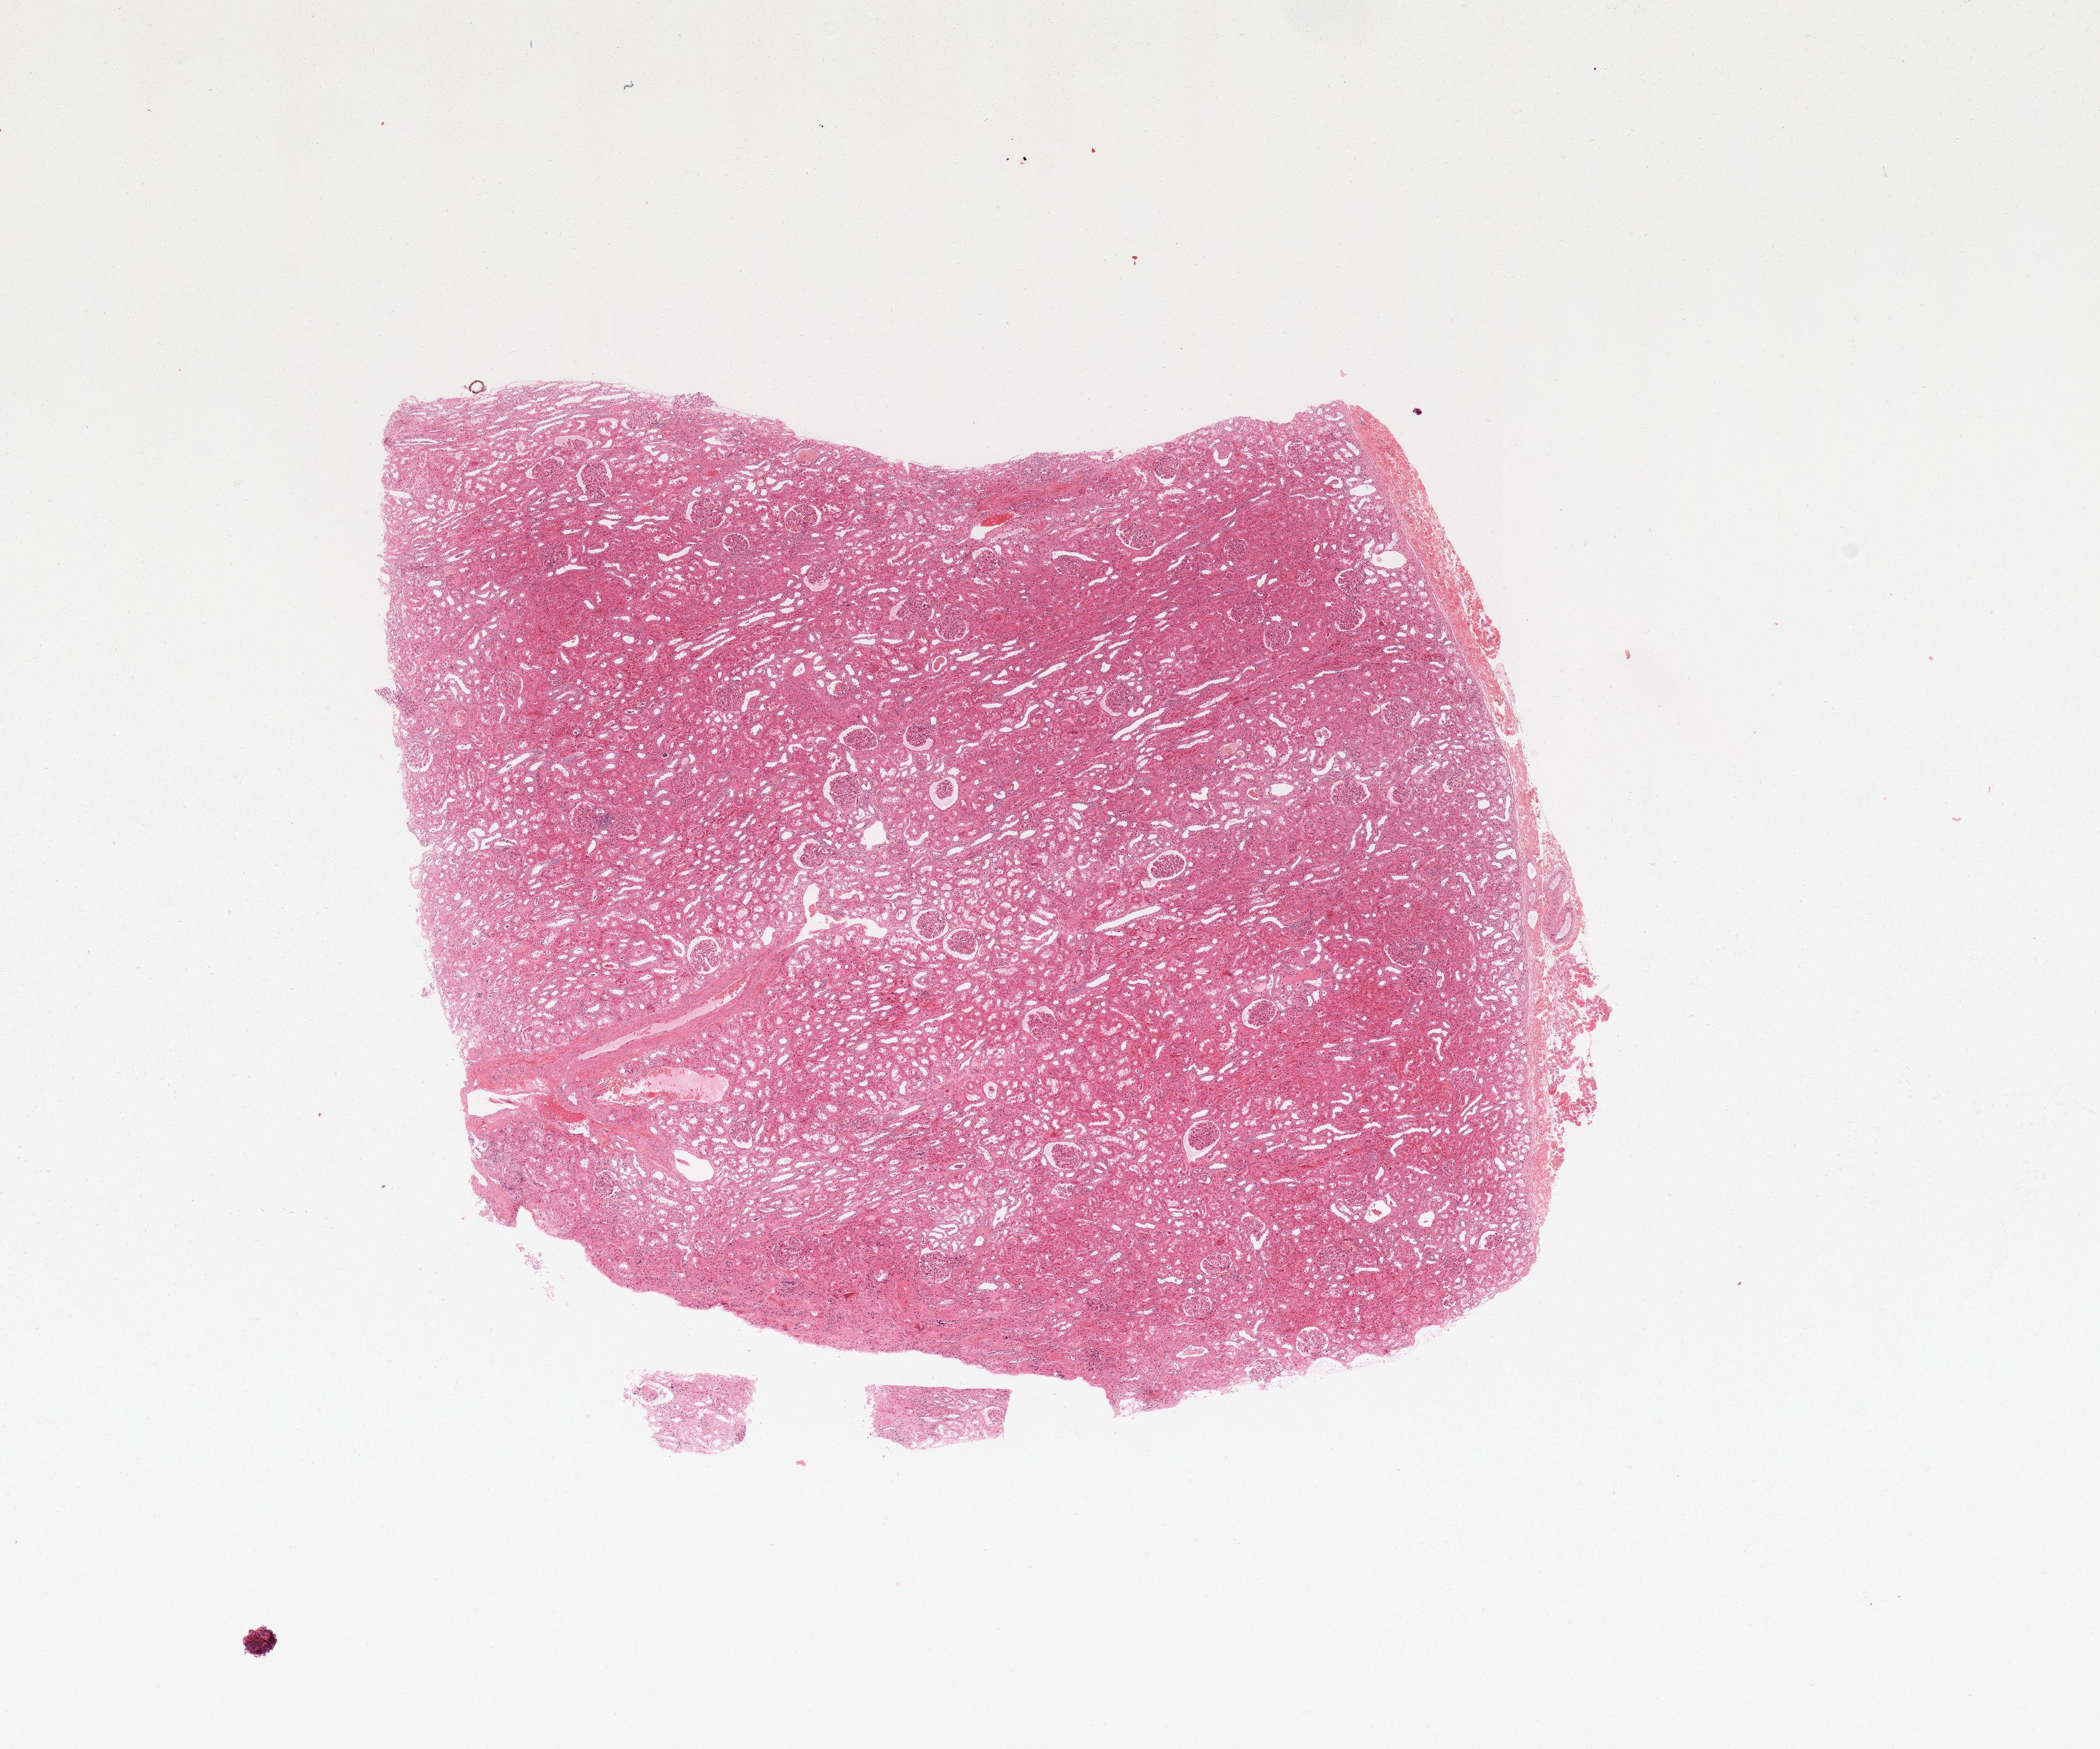
Digitized Hematoxylin and eosin (H&E) stained tissue section (whole slide), whole scanned area (about 13.8 x 11.5 mm, slide scanned at 20x) shown as a low-resolution overview. Normal (non-tumour) tissue sample, sampled site: kidney. 47-year-old male patient.
This section: normal (non-tumour) tissue from the same patient. Patient diagnosis: Renal cell carcinoma, NOS.